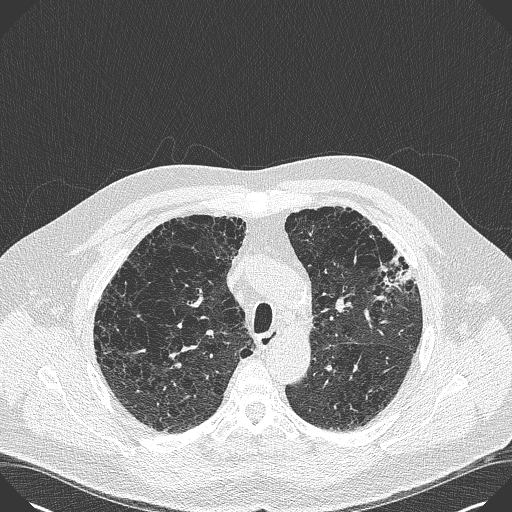
Chest CT (low-dose screening protocol), one axial image; baseline screening round; lung window (W 1500 / L -600 HU); 120 kVp; slice 115 of 383 in the series. Male, age 59 years at enrolment. Current smoker at enrolment.
• Lesion marked by an expert reader, bounding box <374,246,429,297> (left, top, right, bottom; pixels).
• No non-calcified nodule or mass ≥4 mm was recorded by the screening reader at this exam.
• Official screen result: negative screen, minor abnormalities not suspicious for lung cancer.
• Later outcome: lung cancer diagnosed 909 days after this screen — bronchiolo-alveolar carcinoma, mixed mucinous and non-mucinous, left upper lobe, stage IA (AJCC 6th edition), 20 mm at pathology.